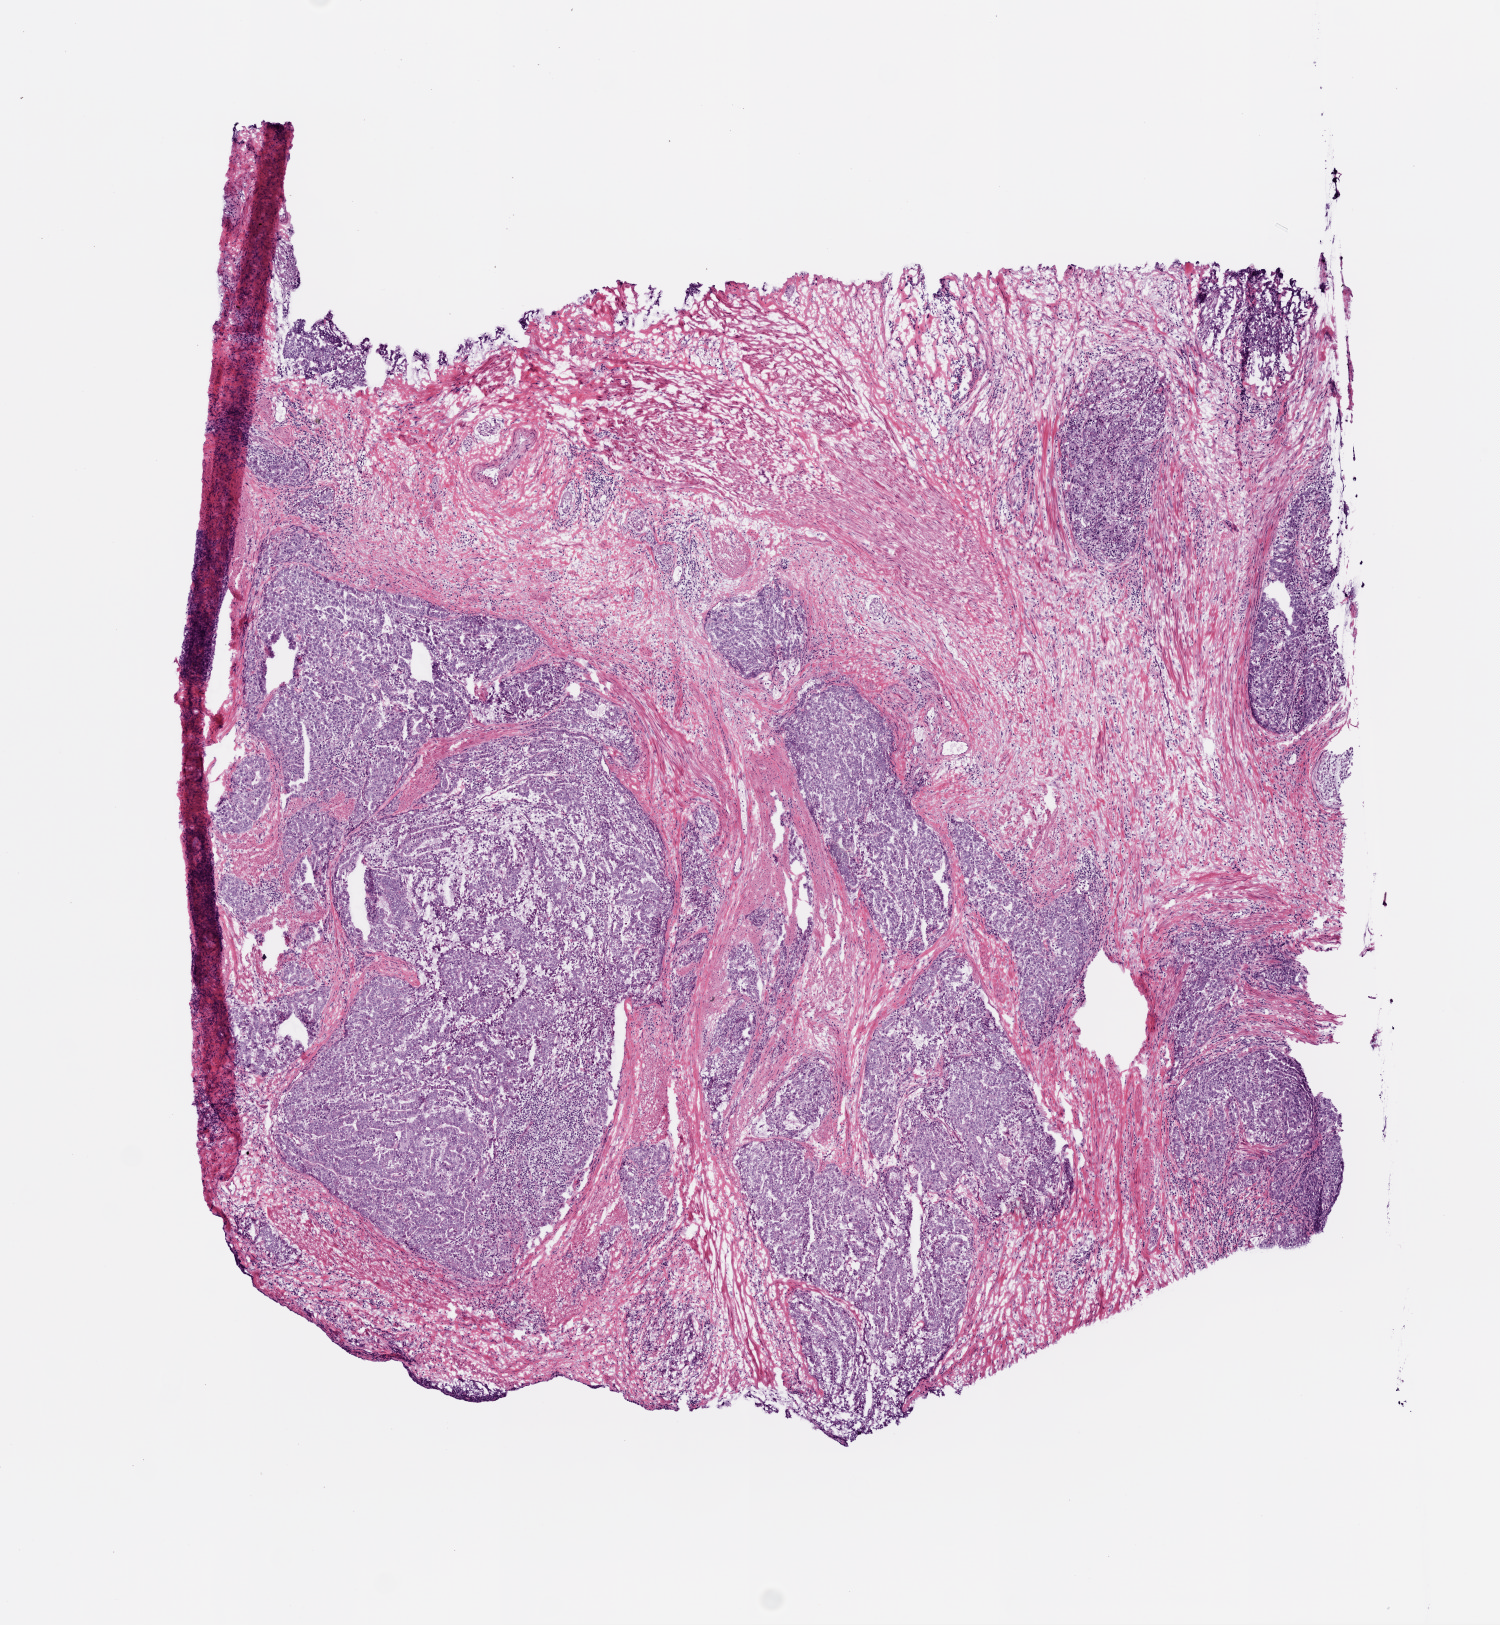
Whole-slide histology image, H&E — low-resolution overview of the scanned area, about 6.0 x 6.5 mm; frozen section from the bottom of the tissue portion; sample: primary tumour, prostate. Patient: male, age at initial diagnosis 65 years. Slide review estimates, as recorded: tumour cells 58%, tumour nuclei 75%.
Pathologic diagnosis: Acinar cell carcinoma (prostate gland).